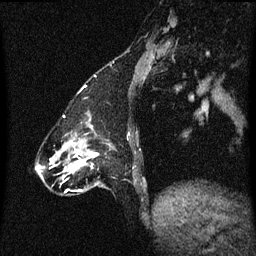
Breast MRI (dynamic contrast-enhanced), one sagittal slice. Position 14 of 60 along the scan axis. Dynamic contrast-enhanced series, image 2 of 3 at this slice position (ordered by acquisition). 1.5 T. TE 4.2 ms, TR 8.4 ms. 256 × 256 image matrix, field of view 200 × 200 mm. Patient: female, 47 years.
Structures marked on this image (semi-automatically segmented with operator editing):
- analysis volume of interest (the breast-tissue region the enhancement analysis was run in; not a lesion): box from (x=81, y=144) to (x=112, y=193) px
- tumour enhancement mask (voxels above the 70 % enhancement threshold inside the analysis volume of interest): (x=90, y=154)–(x=94, y=157)